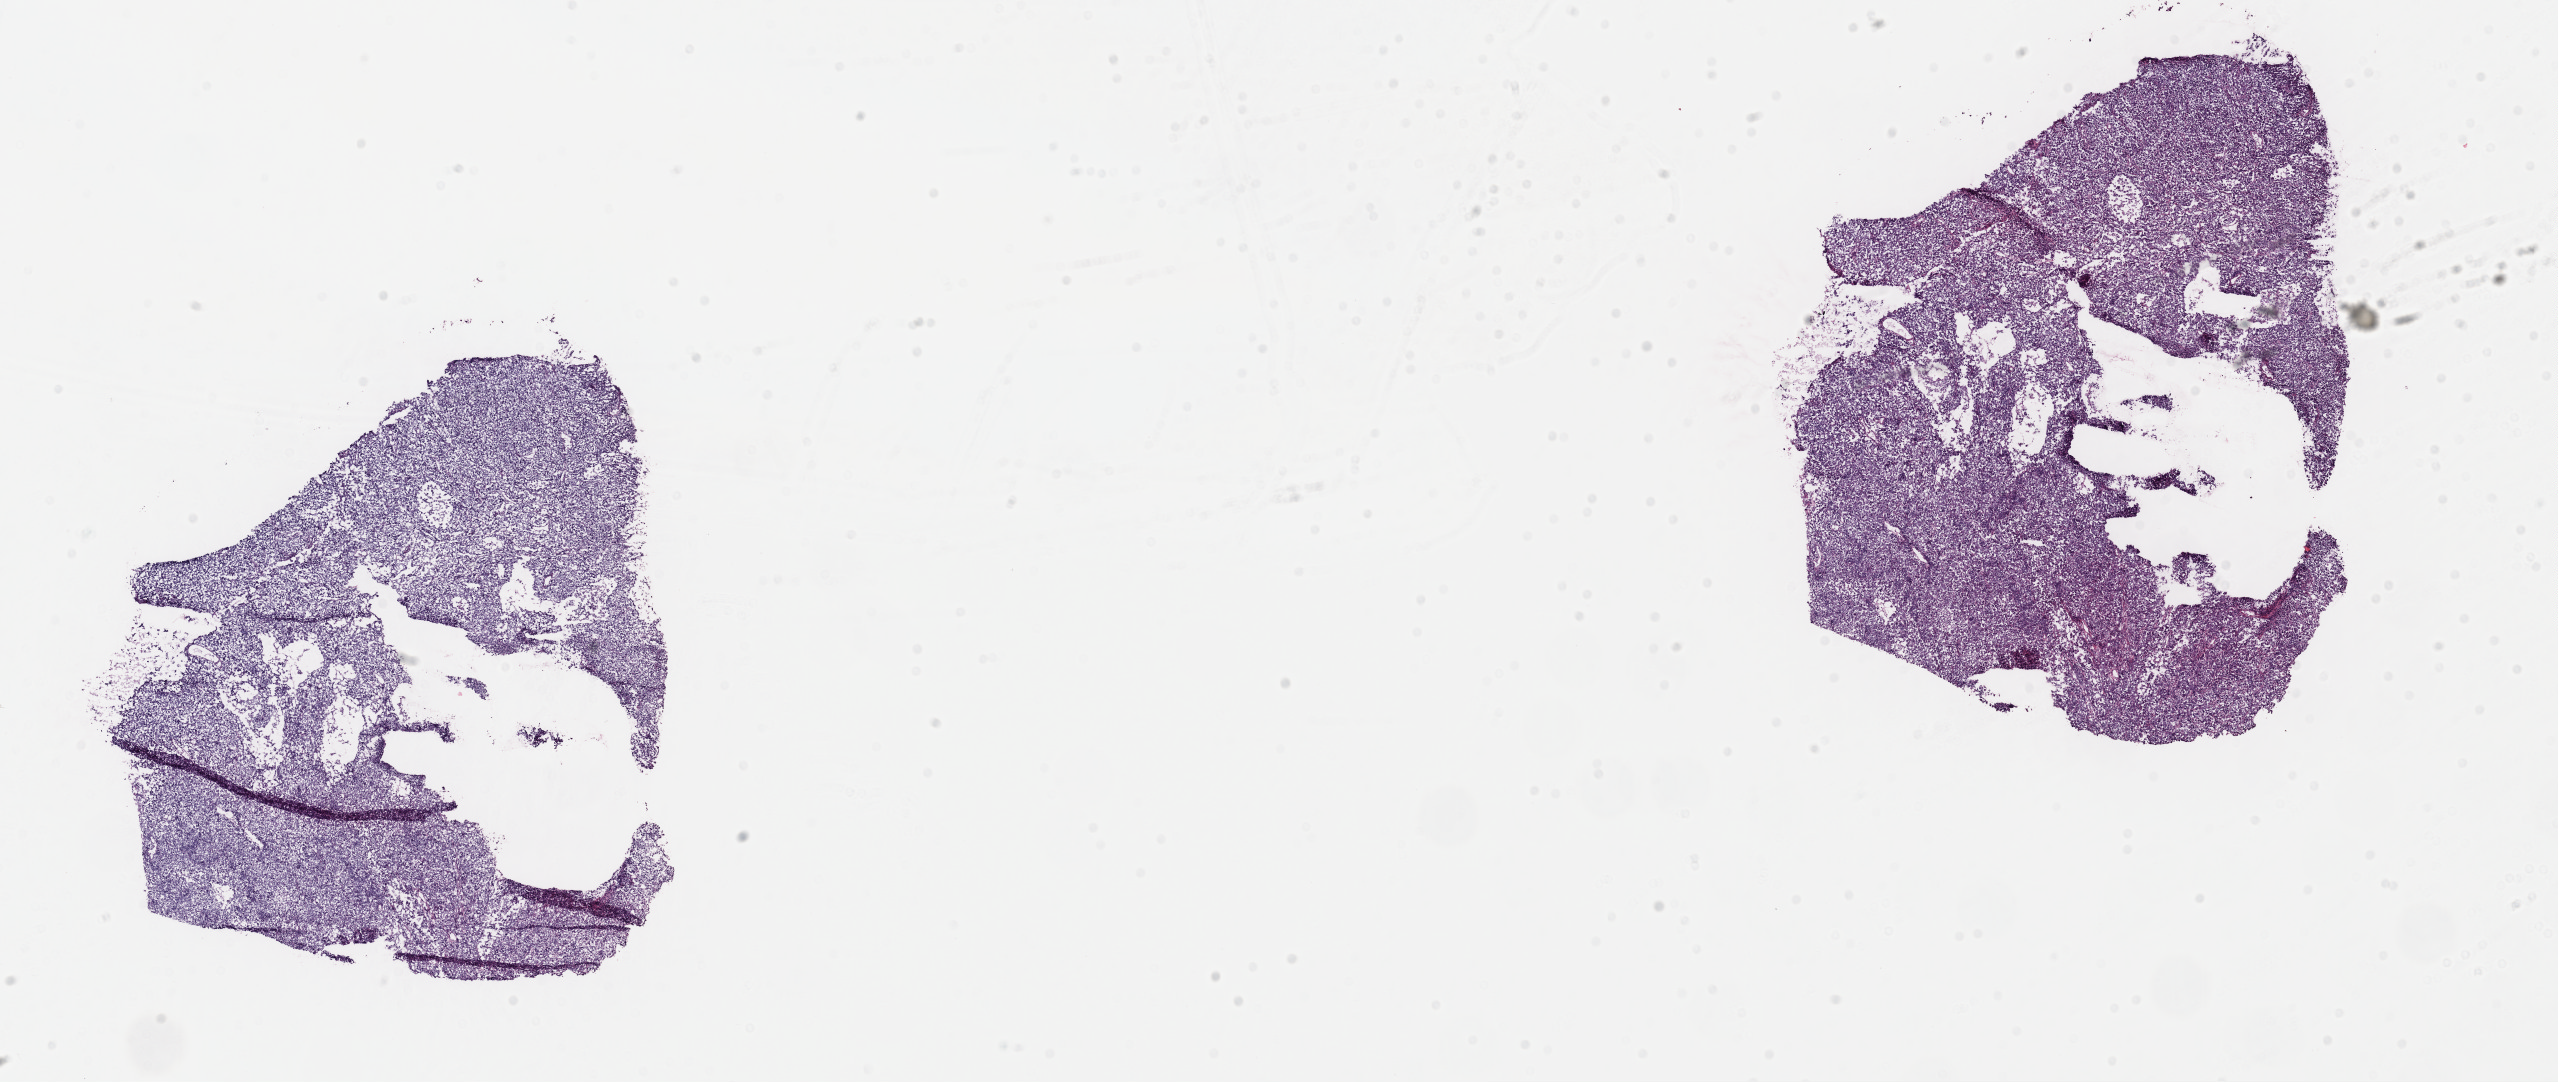
H&E-stained whole-slide image — a low-resolution overview of the entire scanned area, about 20.2 x 8.5 mm; frozen section from the top of the tissue portion; cervix, primary tumour sample. Female patient; age at initial diagnosis 43 years.
Diagnosis: Squamous cell carcinoma, large cell, nonkeratinizing, NOS (cervix uteri).